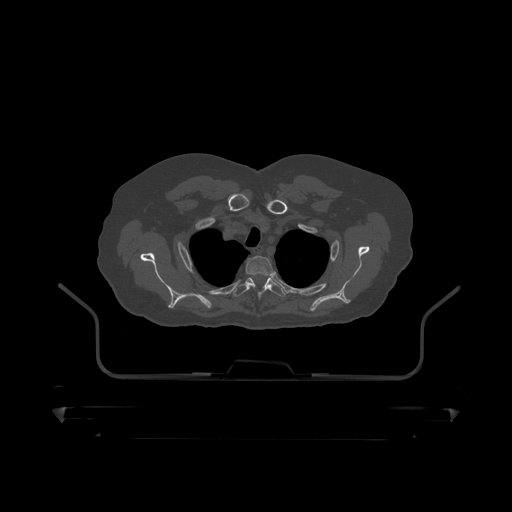
CT including the spine, one axial slice; slice 366 of 390 in the series (ordered by position); reconstruction kernel STANDARD; 120 kVp; bone window (W 1800 / L 400 HU); 512 × 512 image matrix. Patient: male, 60 years. From the clinical record (not read from this slice): primary cancer: prostate.
Outlined on this slice (semi-automatic segmentation, software-assisted and operator-edited):
- T2 vertebra: bounding box (x1, y1, x2, y2) in pixels: (246, 256, 275, 278)
- T3 vertebra: (233, 277, 286, 317)